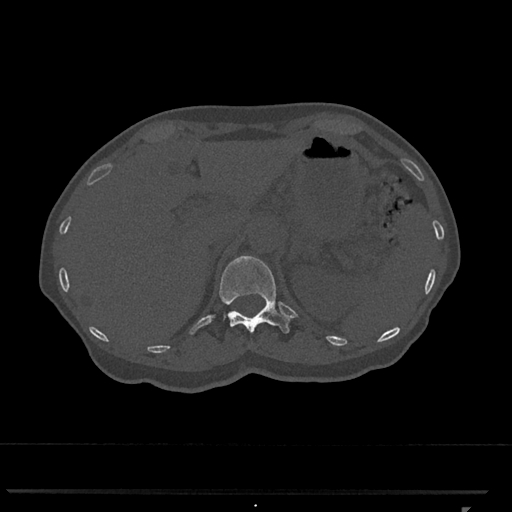
CT including the spine, one axial slice. Slice 460 of 793 in the series (ordered by position). Reconstruction kernel Br40s/3. Bone window (W 1800 / L 400 HU). 512 × 512 image matrix, field of view 380 × 380 mm. Female patient, age 62 years. Case-level facts recorded for this patient, not image findings: primary cancer: renal.
Structures marked on this image (semi-automatic segmentation, software-assisted and operator-edited):
- T12 vertebra: bounding box (x1, y1, x2, y2) in pixels: (219, 256, 291, 334)